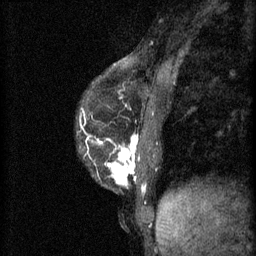
Breast MRI (dynamic contrast-enhanced), one sagittal slice; position 21 of 60 along the scan axis; 3 images stored at this slice position (order not interpretable as contrast timing); 1.5 T; TE 4.2 ms, TR 11 ms; 2 mm slice thickness; 256 × 256 image matrix, field of view 180 × 180 mm. Patient: female, 37 years.
Annotated regions visible in this slice (semi-automatically segmented with operator editing):
- analysis volume of interest (the breast-tissue region the enhancement analysis was run in; not a lesion): bounding box [x1, y1, x2, y2] px = [79, 118, 158, 191]
- tumour enhancement mask (voxels above the 70 % enhancement threshold inside the analysis volume of interest): [98, 136, 138, 185]